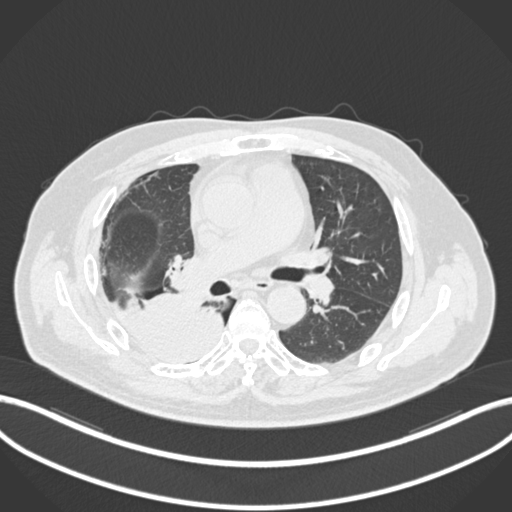
Chest CT, one axial slice. Position 108 of 218 along the scan axis. 120 kVp. Lung window (W 1500 / L -600 HU). 1 mm slice thickness. 512 × 512 image matrix, field of view 400 × 400 mm. Patient: male, 68 years. From the clinical record (not read from this slice): clinical TNM (as recorded): T2a N0 M0.
Outlined on this slice (rectangle marked by the reading radiologist):
- lung tumour (recorded histology: adenocarcinoma): box from (x=110, y=293) to (x=231, y=368) px